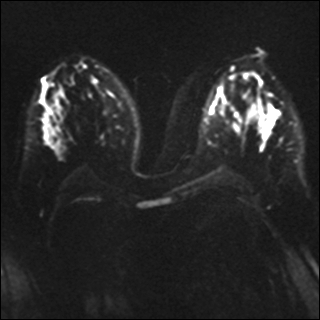
Breast MRI, one axial slice. Slice 18 of 41 in the series (ordered by position). Diffusion-weighted series; image 2 of 4 stored at this slice position (different b-values; order by instance number). 1.5 T. 4 mm slice thickness. 320 × 320 image matrix, field of view 340 × 340 mm. Female patient.
Outlined on this slice (outlined manually by an expert reader):
- tumour on diffusion-weighted imaging: box from (x=264, y=117) to (x=273, y=135) px